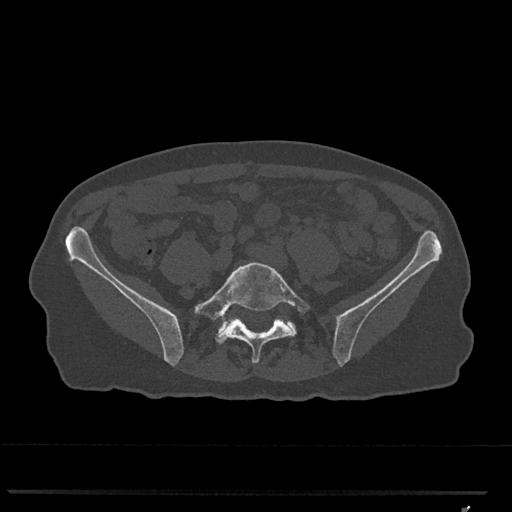
CT including the spine, one axial slice; slice 146 of 793 in the series (ordered by position); reconstruction kernel Br40s/3; 120 kVp; bone window (W 1800 / L 400 HU); 512 × 512 image matrix. Patient: female, 62 years. From the clinical record (not read from this slice): primary cancer: renal.
Outlined on this slice (semi-automatically segmented with operator editing):
- L5 vertebra: bounding box (x1, y1, x2, y2) in pixels: (194, 262, 312, 363)